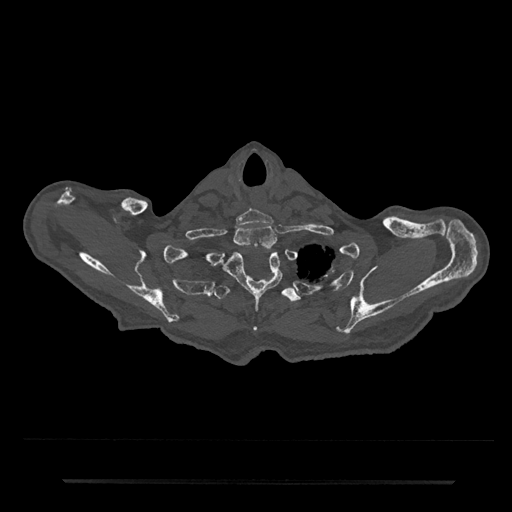
CT including the spine, one axial slice; 120 kVp; bone window (W 1800 / L 400 HU); 0.5 mm slice thickness; 512 × 512 image matrix. Patient: male, 74 years. Case-level facts recorded for this patient, not image findings: primary cancer: prostate.
Structures marked on this image (semi-automatically segmented with operator editing):
- T1 vertebra: bounding box (x1, y1, x2, y2) in pixels: (234, 225, 277, 250)
- T2 vertebra: (218, 250, 283, 330)
- T3 vertebra: (214, 272, 301, 302)